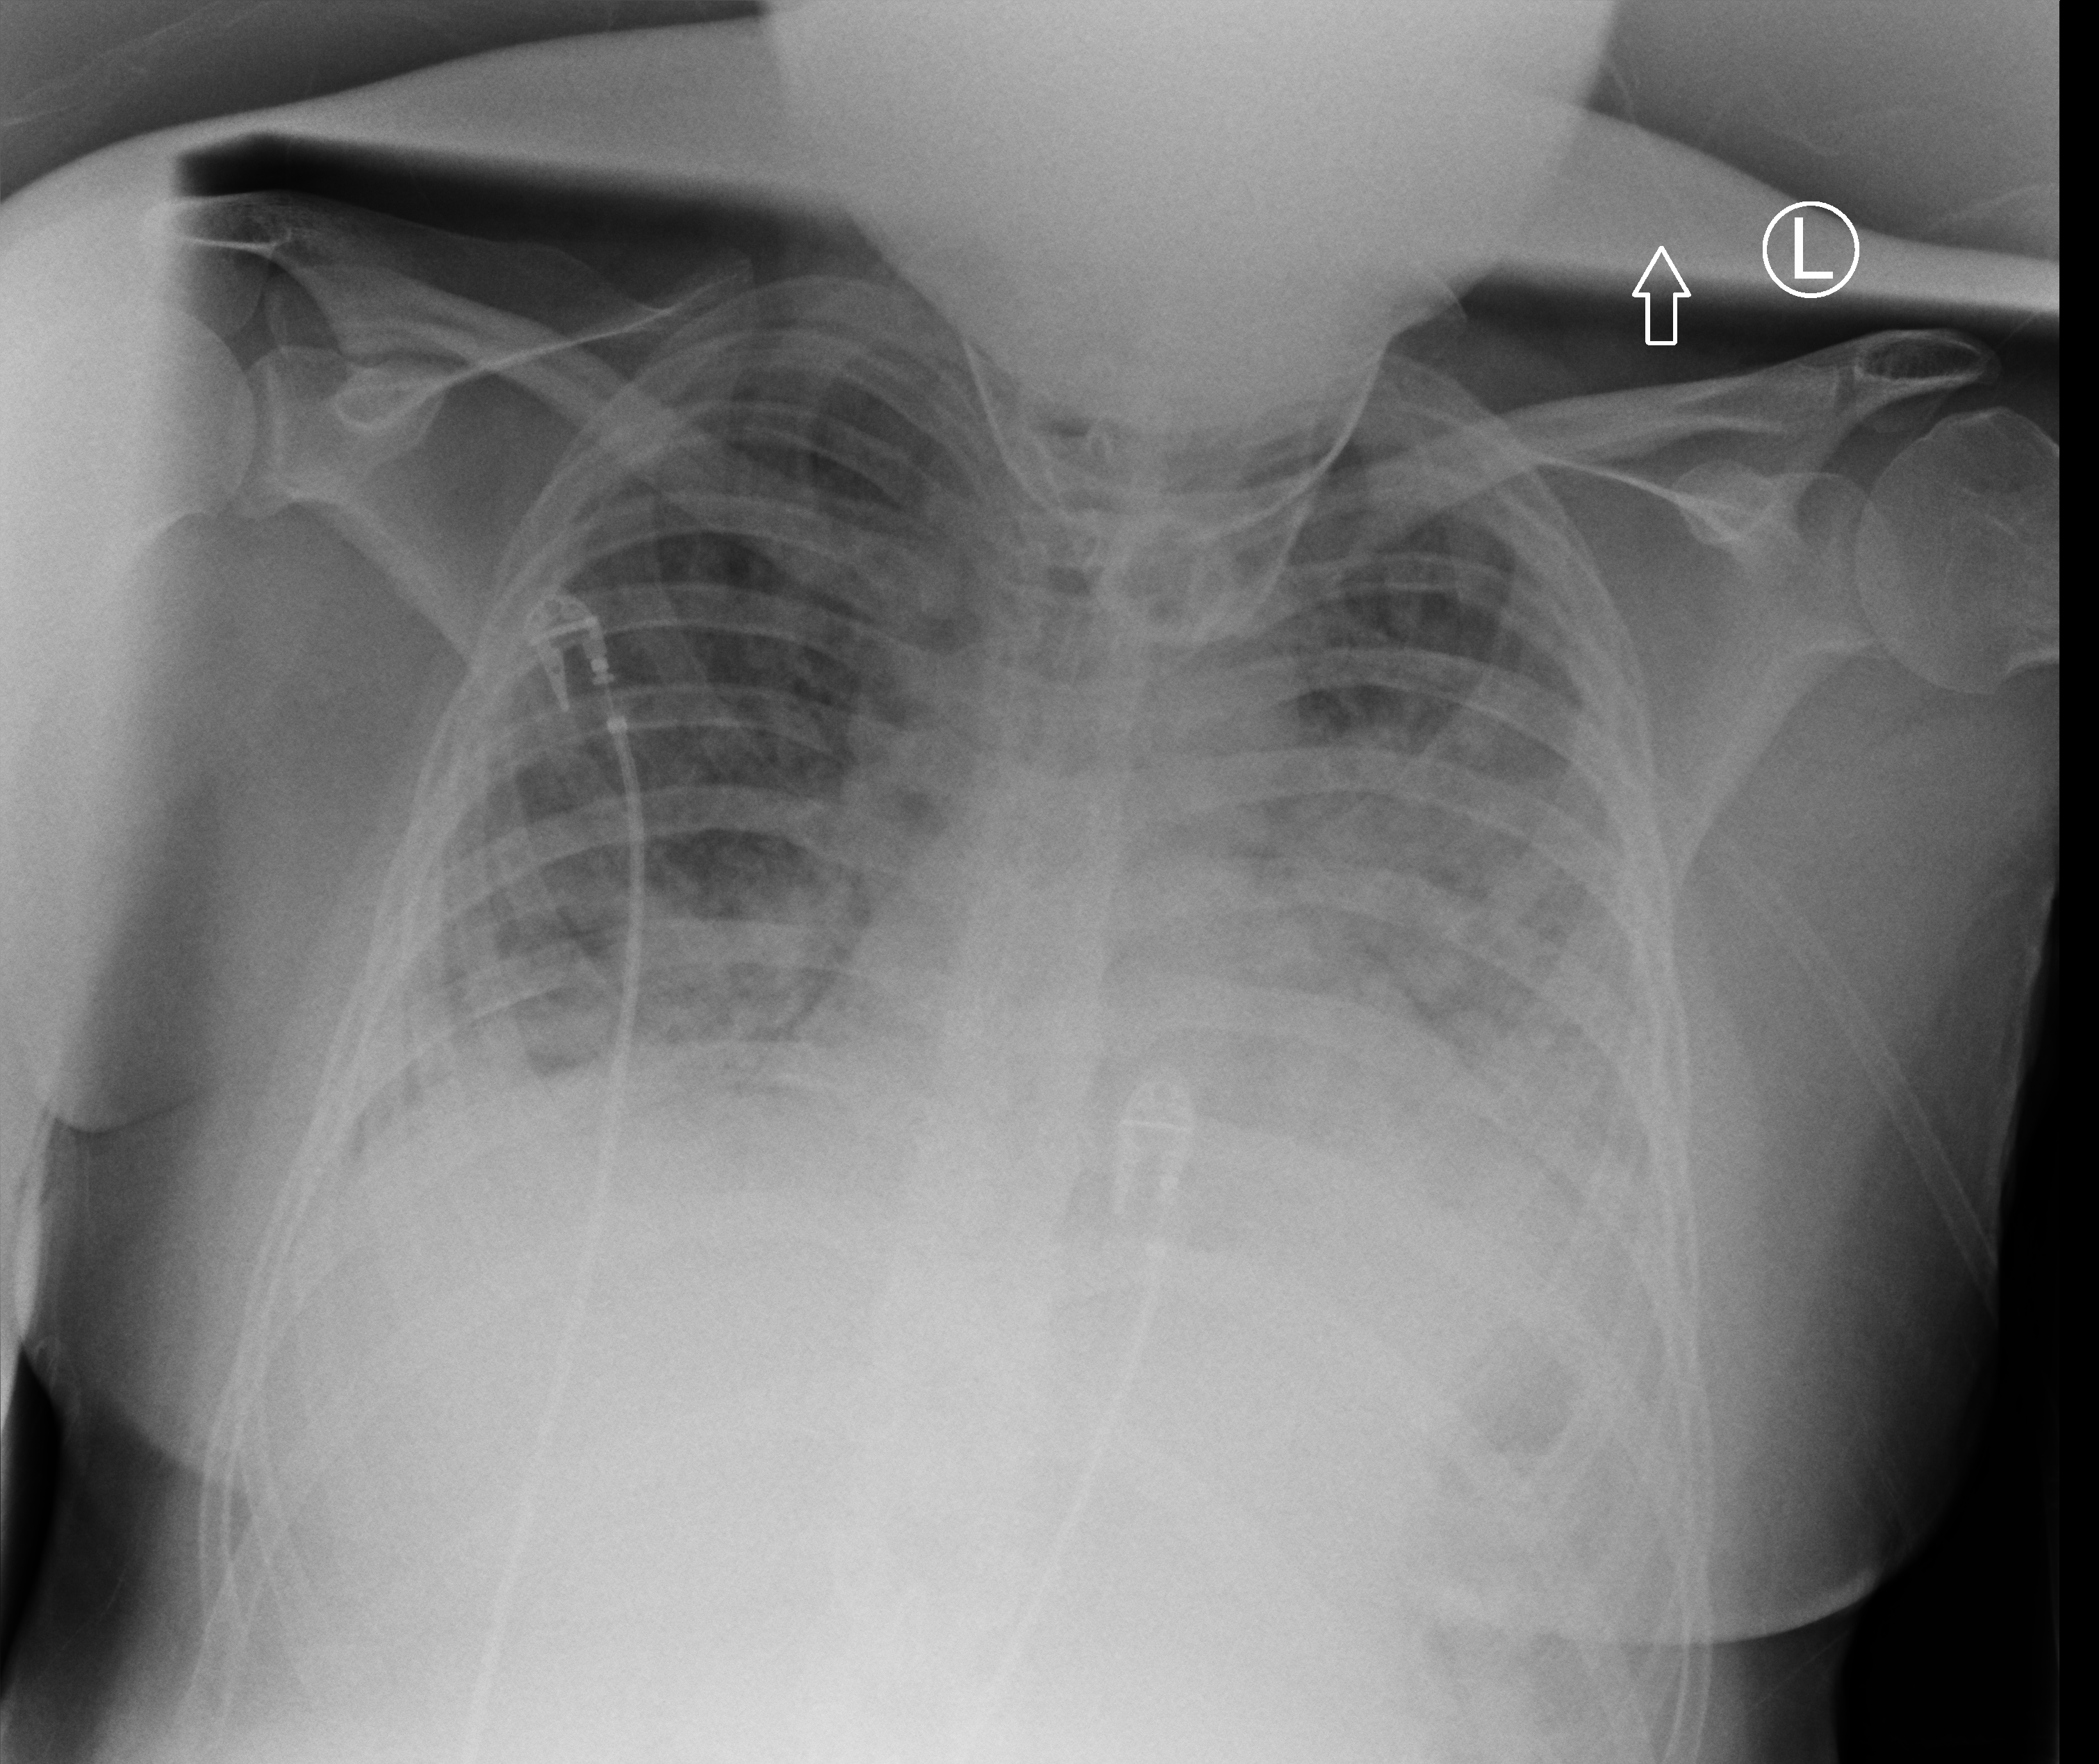
Portable chest radiograph; anteroposterior (AP) projection. Male patient hospitalised with COVID-19, age 18–59 years.
Admission-level facts for this patient (not findings on this image; timing relative to this image not recorded): other chronic lung disease (admission record): no; mechanically ventilated during this hospital stay: no.